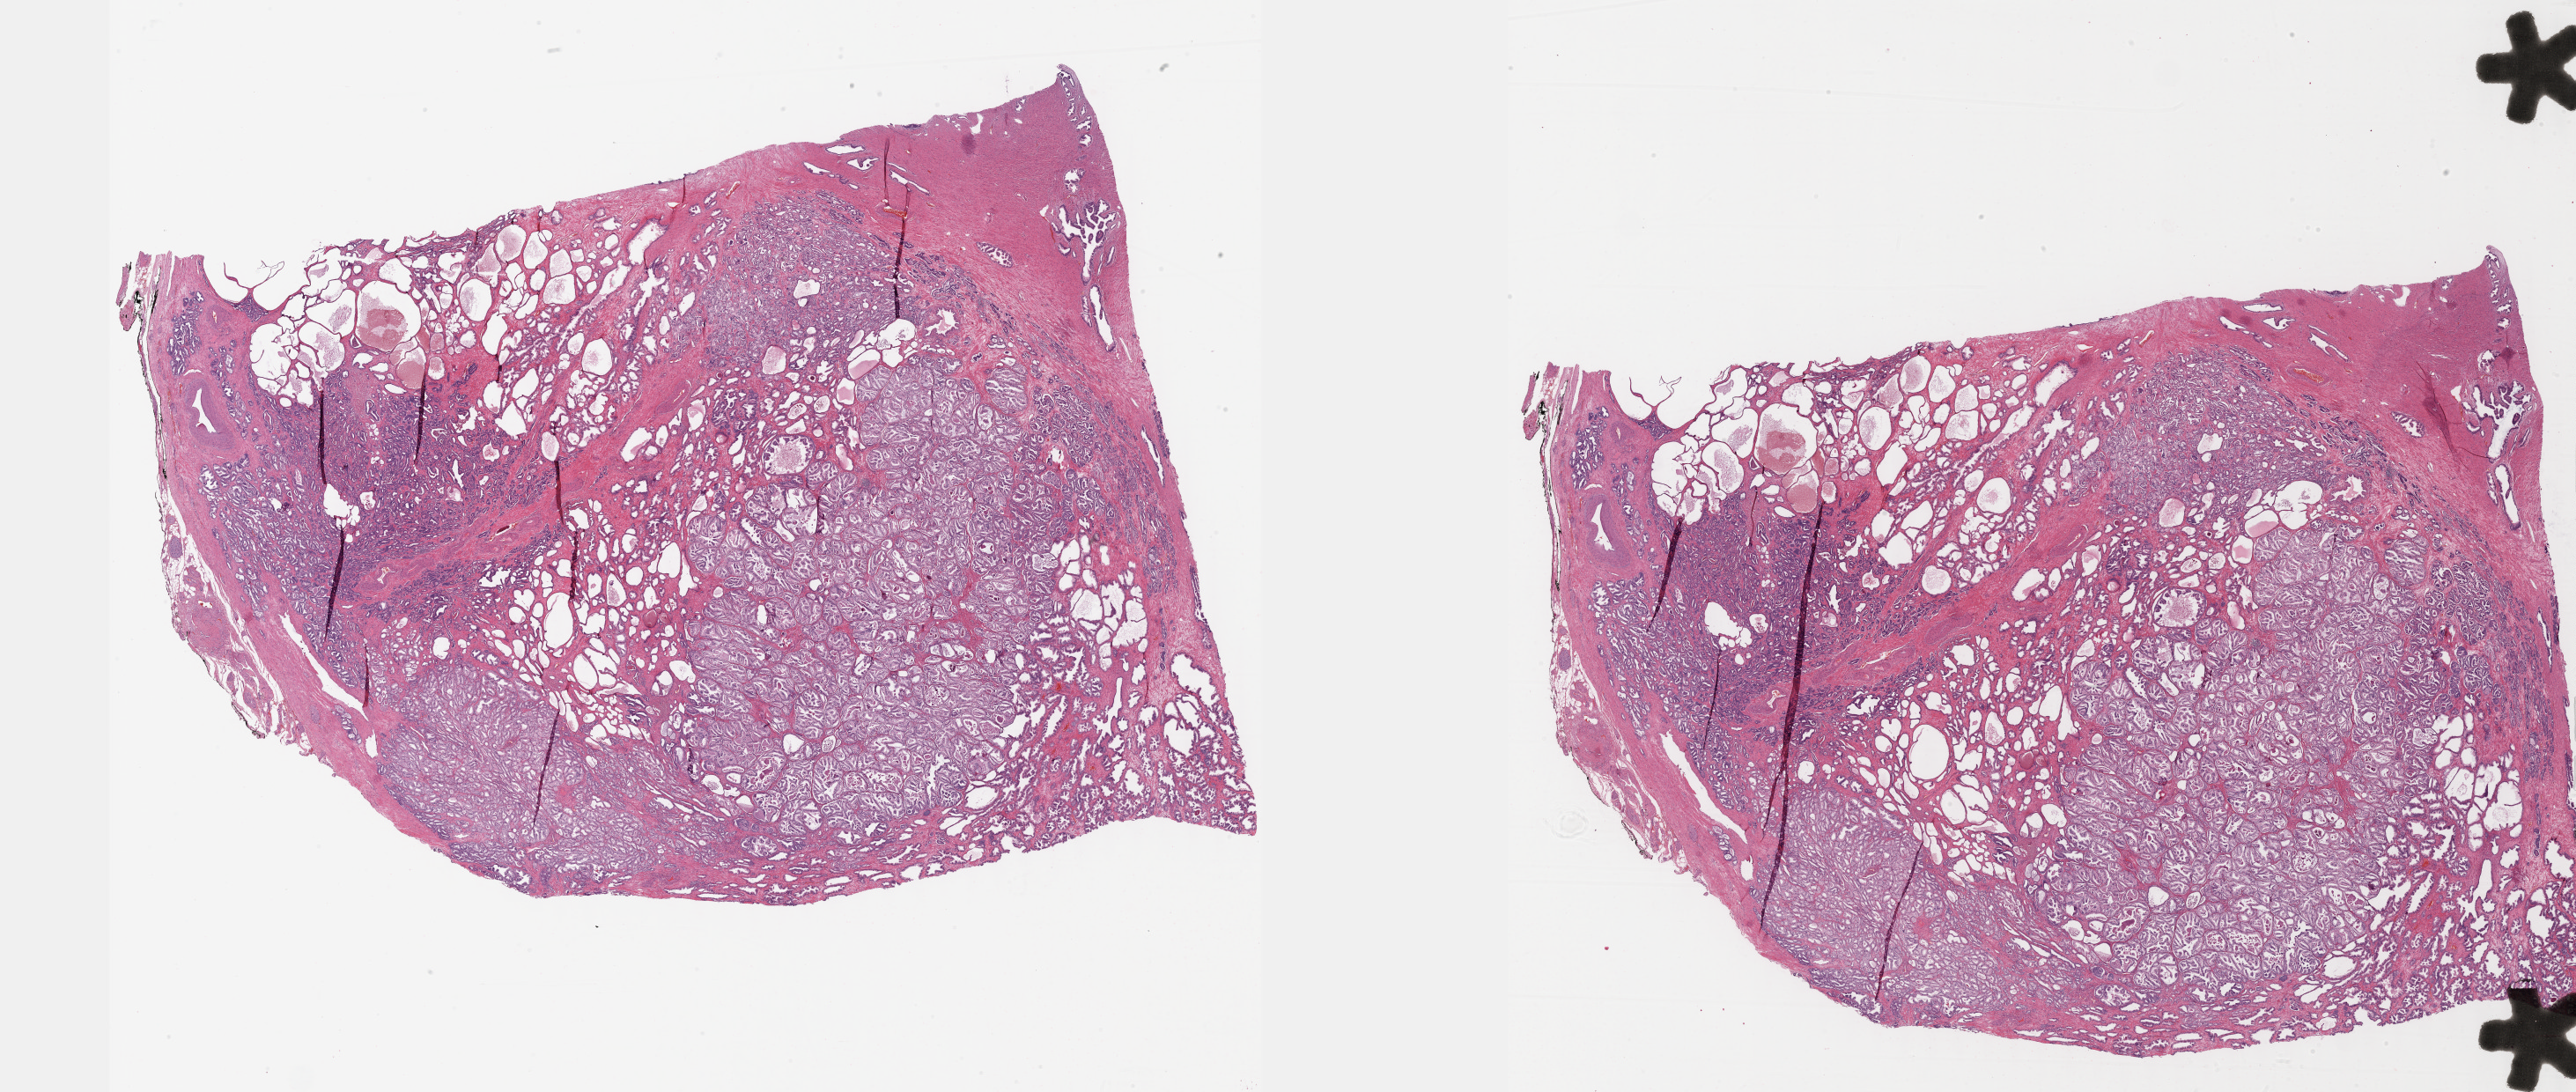
Whole-slide histology image, Hematoxylin and eosin (H&E) stained — shown as a low-resolution overview of the whole scanned area (about 47.3 x 20.0 mm, from a 40x scan), formalin-fixed paraffin-embedded (FFPE) diagnostic section, sample: primary tumour, prostate. Male patient; age at initial diagnosis 59 years. Gleason score: 7 (3+4).
• diagnosis: Adenocarcinoma, NOS (prostate gland)
• laterality: bilateral